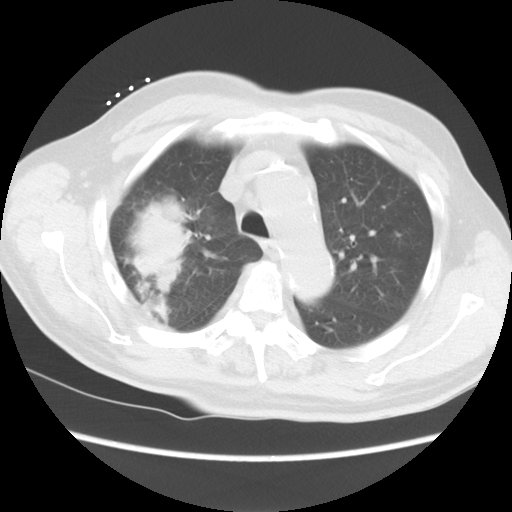
Chest CT, one axial slice; position 14 of 15 along the scan axis; reconstruction kernel STANDARD; 120 kVp; lung window (W 1500 / L -600 HU); 5 mm slice thickness; 512 × 512 image matrix, field of view 350 × 350 mm. Patient: male, 68 years. From the clinical record (not read from this slice): clinical TNM (as recorded): T4 N3 M0.
Outlined on this slice (rectangle marked by the reading radiologist):
- lung tumour (recorded histology: squamous cell carcinoma): box from (x=134, y=203) to (x=204, y=296) px